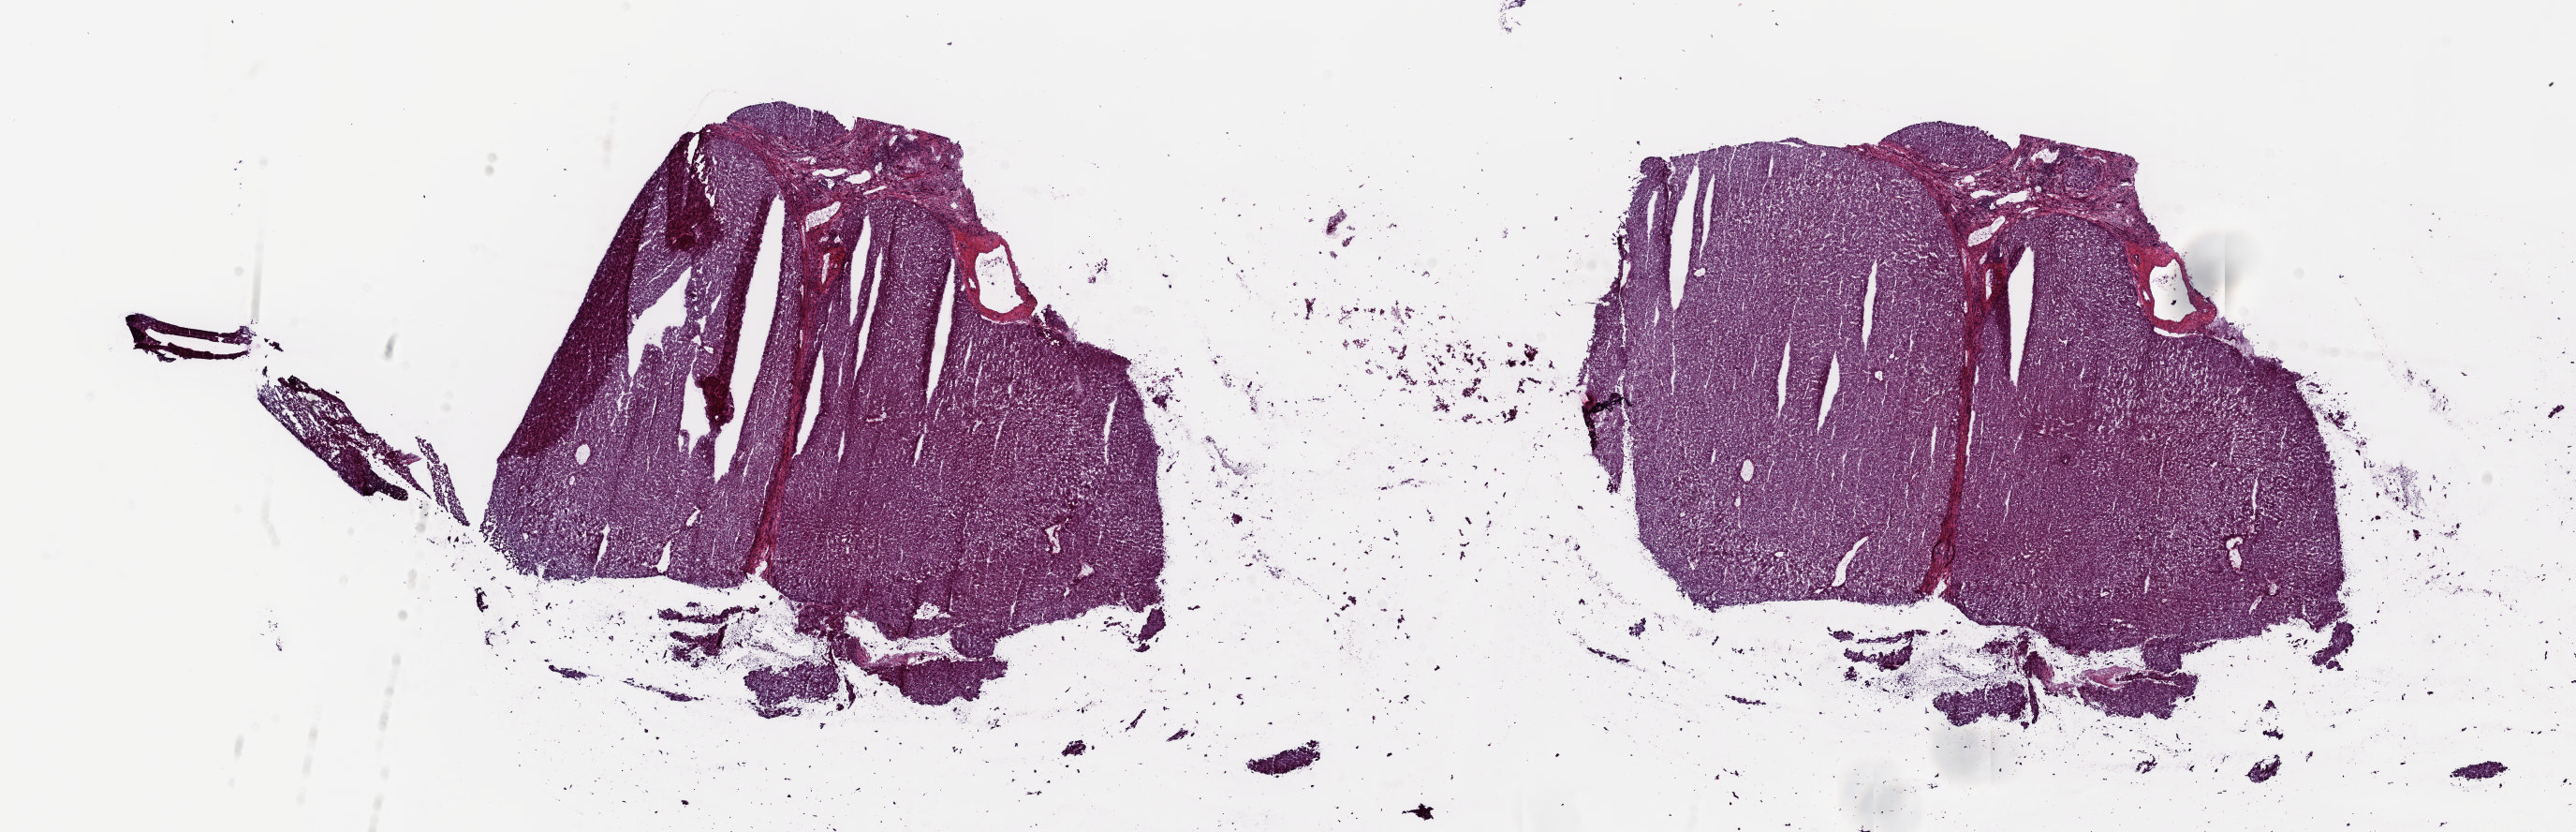
Digitized H&E-stained tissue section (whole slide), whole scanned area (about 21.8 x 7.0 mm) shown as a low-resolution overview; frozen section from the top of the tissue portion; sample: solid tissue normal (non-tumour tissue), liver. Male, age 46 years at initial diagnosis. Pathologist review of this section (percent, as recorded): tumour cells 0%, tumour nuclei 0%.
This section: solid tissue normal sample (biorepository sample class). Patient diagnosis: Hepatocellular carcinoma, NOS.